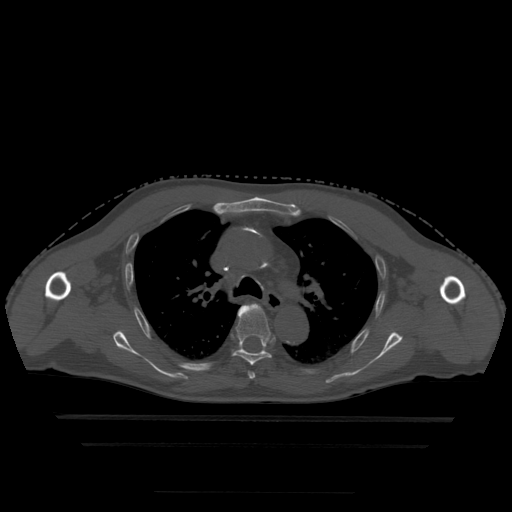
CT including the spine, one axial slice. Position 338 of 522 along the scan axis. Bone window (W 1800 / L 400 HU). 1.25 mm slice thickness. 512 × 512 image matrix, field of view 436 × 436 mm. Patient age 68 years. Case-level facts recorded for this patient, not image findings: primary cancer: urothelial.
Outlined on this slice (semi-automatically segmented with operator editing):
- T4 vertebra: bounding box <246,306,255,380> (left, top, right, bottom; pixels)
- T5 vertebra: <233,304,271,366>